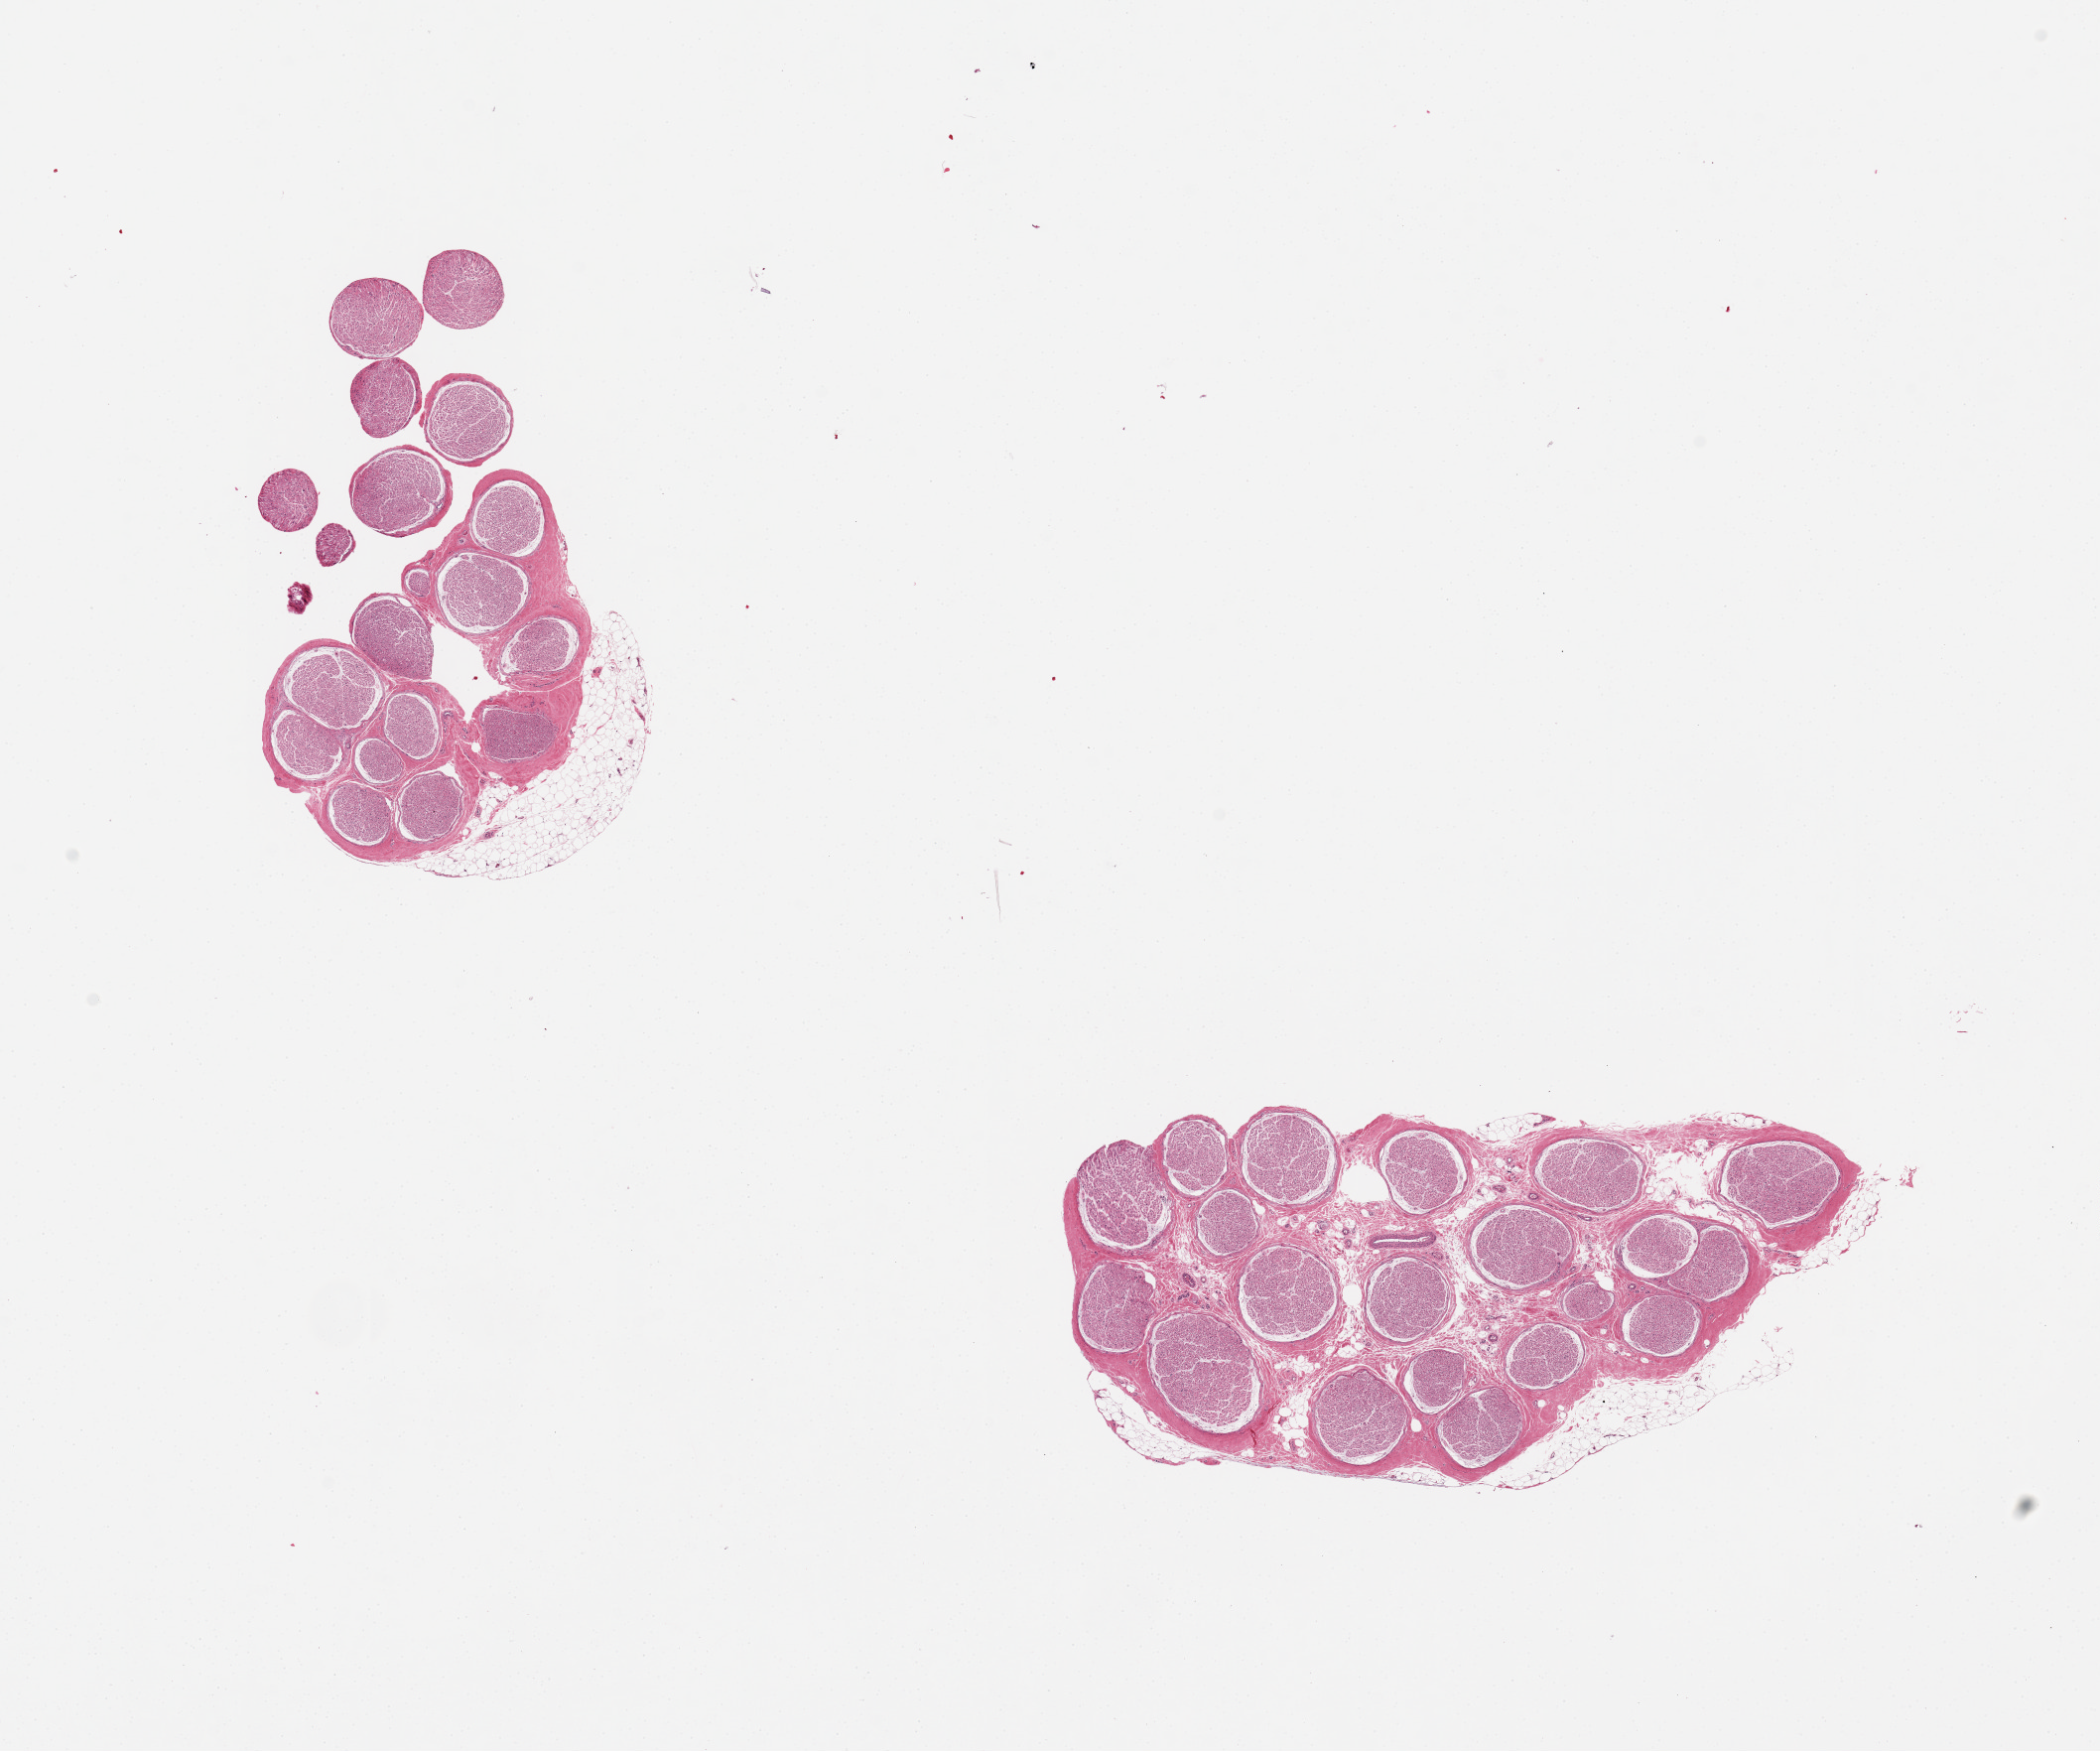
Hematoxylin and eosin (H&E) whole-slide image, shown as a low-resolution overview of the whole scanned area (about 16.7 x 14.0 mm, from a 20x scan), PAXgene-fixed, paraffin-embedded tissue, section of tibial nerve (target tissue), donor tissue sample. Donor: male.
Reviewer comment on this tissue sample: 2 pieces. Well trimmed. Small amount of peripheral fat.